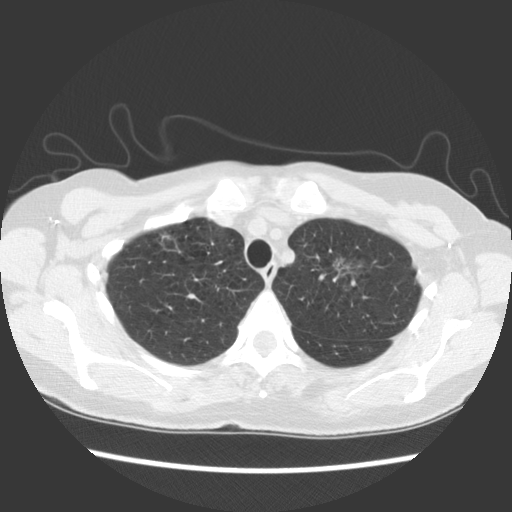
Chest CT (low-dose screening protocol), one axial image; baseline annual screen; lung window (W 1500 / L -600 HU); 2.5 mm slice thickness; standard (soft-tissue) reconstruction kernel (STANDARD). Female, age 65 years at enrolment. Former smoker at enrolment.
Expert reader's lesion annotation, bounding box [x1, y1, x2, y2] px = [311, 241, 380, 298]. Reader record for this screening exam (exam-level; its link to the box is not recorded): non-calcified nodule or mass ≥4 mm, left upper lobe, 11 × 10 mm, poorly defined margins, ground glass attenuation. Official screen result: positive, change unspecified: nodule(s) >= 4 mm or enlarging nodule(s), mass(es), or other non-specific abnormalities suspicious for lung cancer. Participant outcome: lung cancer diagnosed 810 days after this screen — adenocarcinoma, NOS, left upper lobe, moderately differentiated (G2), stage IA (AJCC 6th edition), 30 mm at pathology.